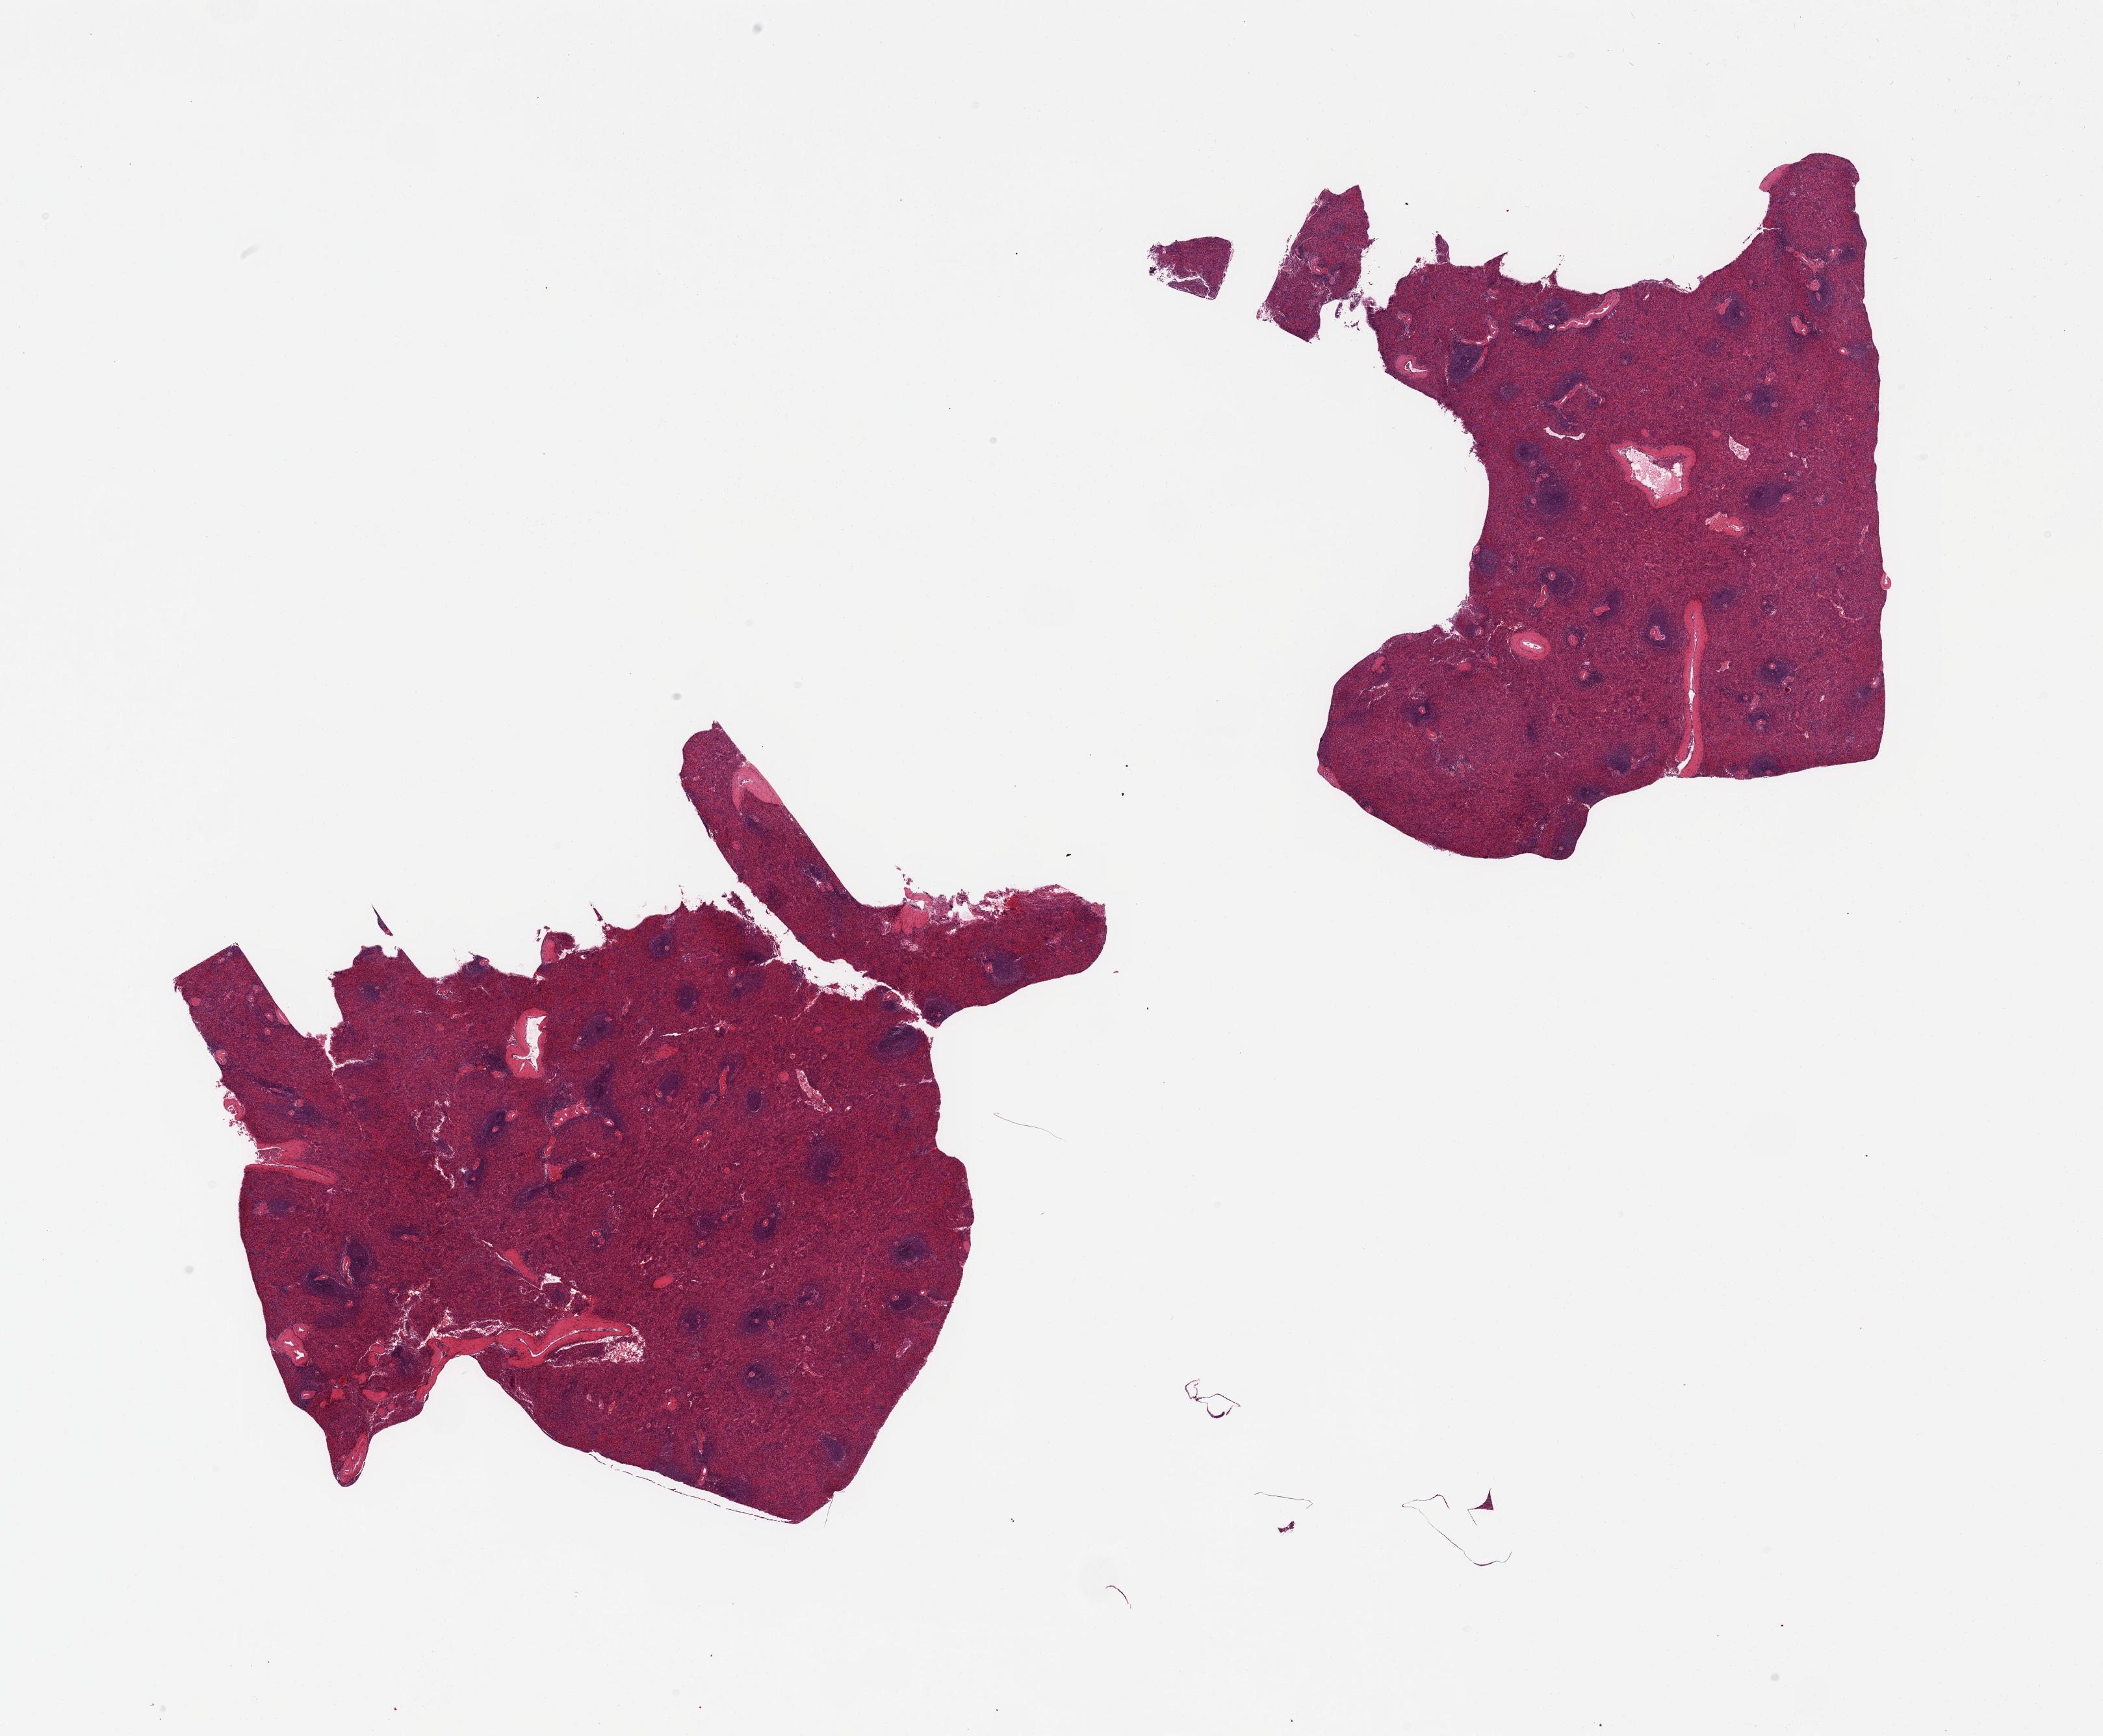
Digitized H&E-stained section, low-resolution overview of the scanned area, about 25.6 x 21.1 mm (from a 20x scan), PAXgene-fixed paraffin-embedded (PFPE) section, sampled site (target tissue): spleen, tissue donor sample. Male donor.
- reviewer comment on this tissue sample: 2 pieces; moderate congestion